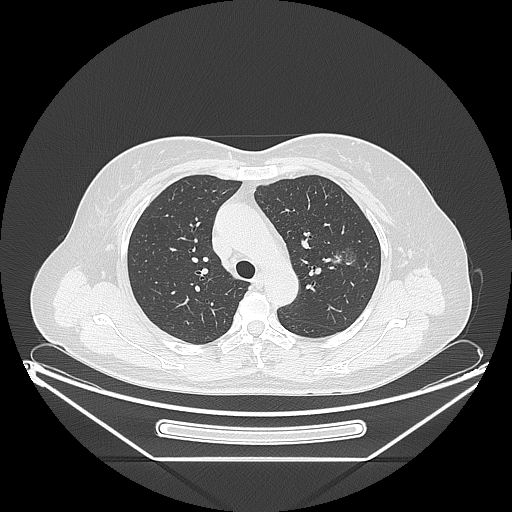
Chest CT, one axial slice. Slice 153 of 226 in the series (ordered by position). Reconstruction kernel LUNG. 120 kVp. Lung window (W 1500 / L -600 HU). 1.25 mm slice thickness. 512 × 512 image matrix. Female patient, age 54 years. Case-level facts recorded for this patient, not image findings: clinical TNM (as recorded): T1c N0 M0; histopathological grade: G1.
Structures marked on this image (bounding box drawn by a radiologist):
- lung tumour (recorded histology: adenocarcinoma): box from (x=322, y=243) to (x=365, y=276) px